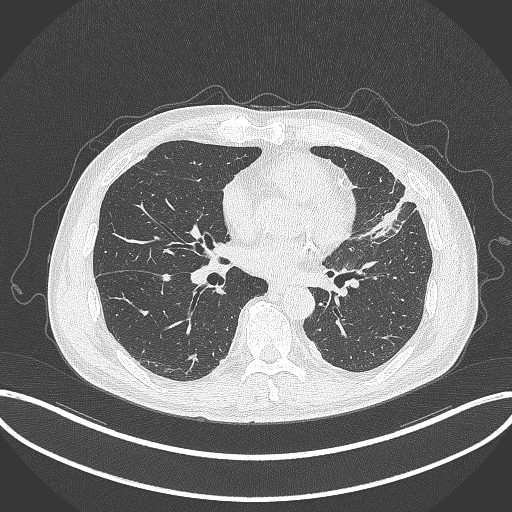
Chest CT, one axial slice. Slice 148 of 382 in the series (ordered by position). Reconstruction kernel B70f. Lung window (W 1500 / L -600 HU). 1 mm slice thickness. 512 × 512 image matrix. Male patient, age 64 years. From the clinical record (not read from this slice): clinical TNM (as recorded): T4 N1 M0.
Structures marked on this image (bounding box drawn by a radiologist):
- lung tumour (recorded histology: adenocarcinoma): bounding box [x1, y1, x2, y2] px = [361, 183, 419, 247]